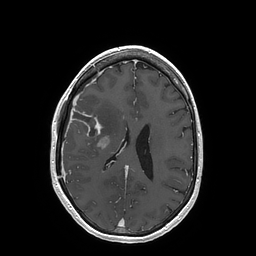
Brain MRI from a brain-tumour surgery series, one axial slice; slice 69 of 202 in the series (ordered by position); T1-weighted post-contrast; 1 mm slice thickness; 256 × 256 image matrix, field of view 250 × 250 mm. From the clinical record (not read from this slice): histopathology: Glioblastoma; WHO grade: 4; IDH mutation: no.
Annotated regions visible in this slice (expert manual segmentation):
- tumour: bounding box <71,108,108,148> (left, top, right, bottom; pixels)